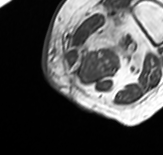
MRI of an extremity soft-tissue mass, one axial slice; slice 9 of 65 in the series (ordered by position); MR volume resampled by the dataset authors to the PET/CT grid (not the native acquisition matrix); 3.27 mm slice thickness; 163 × 155 image matrix, field of view 159 × 151 mm. Female patient. Case-level facts recorded for this patient, not image findings: histological type: pleomorphic leiomyosarcoma; grade: high; site of the primary tumour: left thigh.
Annotated regions visible in this slice (expert contour drawn on MRI and transferred to this co-registered scan by the dataset authors):
- gross tumour volume including surrounding oedema: bounding box <64,8,145,75> (left, top, right, bottom; pixels)